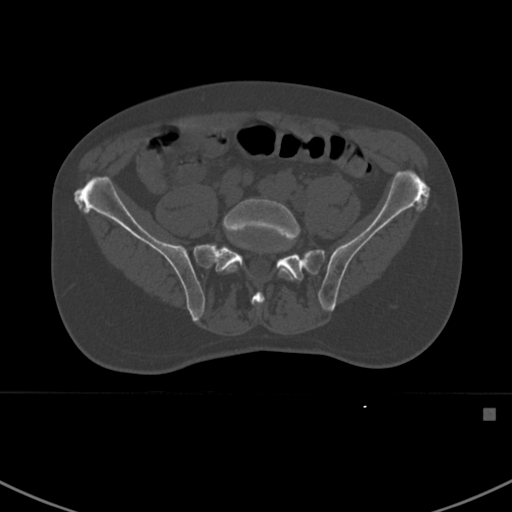
CT including the spine, one axial slice. Slice 210 of 412 in the series (ordered by position). Reconstruction kernel Br40s. Bone window (W 1800 / L 400 HU). 512 × 512 image matrix, field of view 358 × 358 mm. Male patient, age 59 years. Case-level facts recorded for this patient, not image findings: primary cancer: prostate.
Outlined on this slice (semi-automatic segmentation, software-assisted and operator-edited):
- L5 vertebra: bounding box <223,198,299,280> (left, top, right, bottom; pixels)